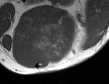
MRI of an extremity soft-tissue mass, one axial slice; position 38 of 50 along the scan axis; MR volume resampled by the dataset authors to the PET/CT grid (not the native acquisition matrix); 109 × 84 image matrix. Male patient. Case-level facts recorded for this patient, not image findings: histological type: synovial sarcoma; site of the primary tumour: left poplietal fossa.
Outlined on this slice (expert contour drawn on MRI and transferred to this co-registered scan by the dataset authors):
- gross tumour volume (mass): bounding box (x1, y1, x2, y2) in pixels: (32, 25, 65, 63)